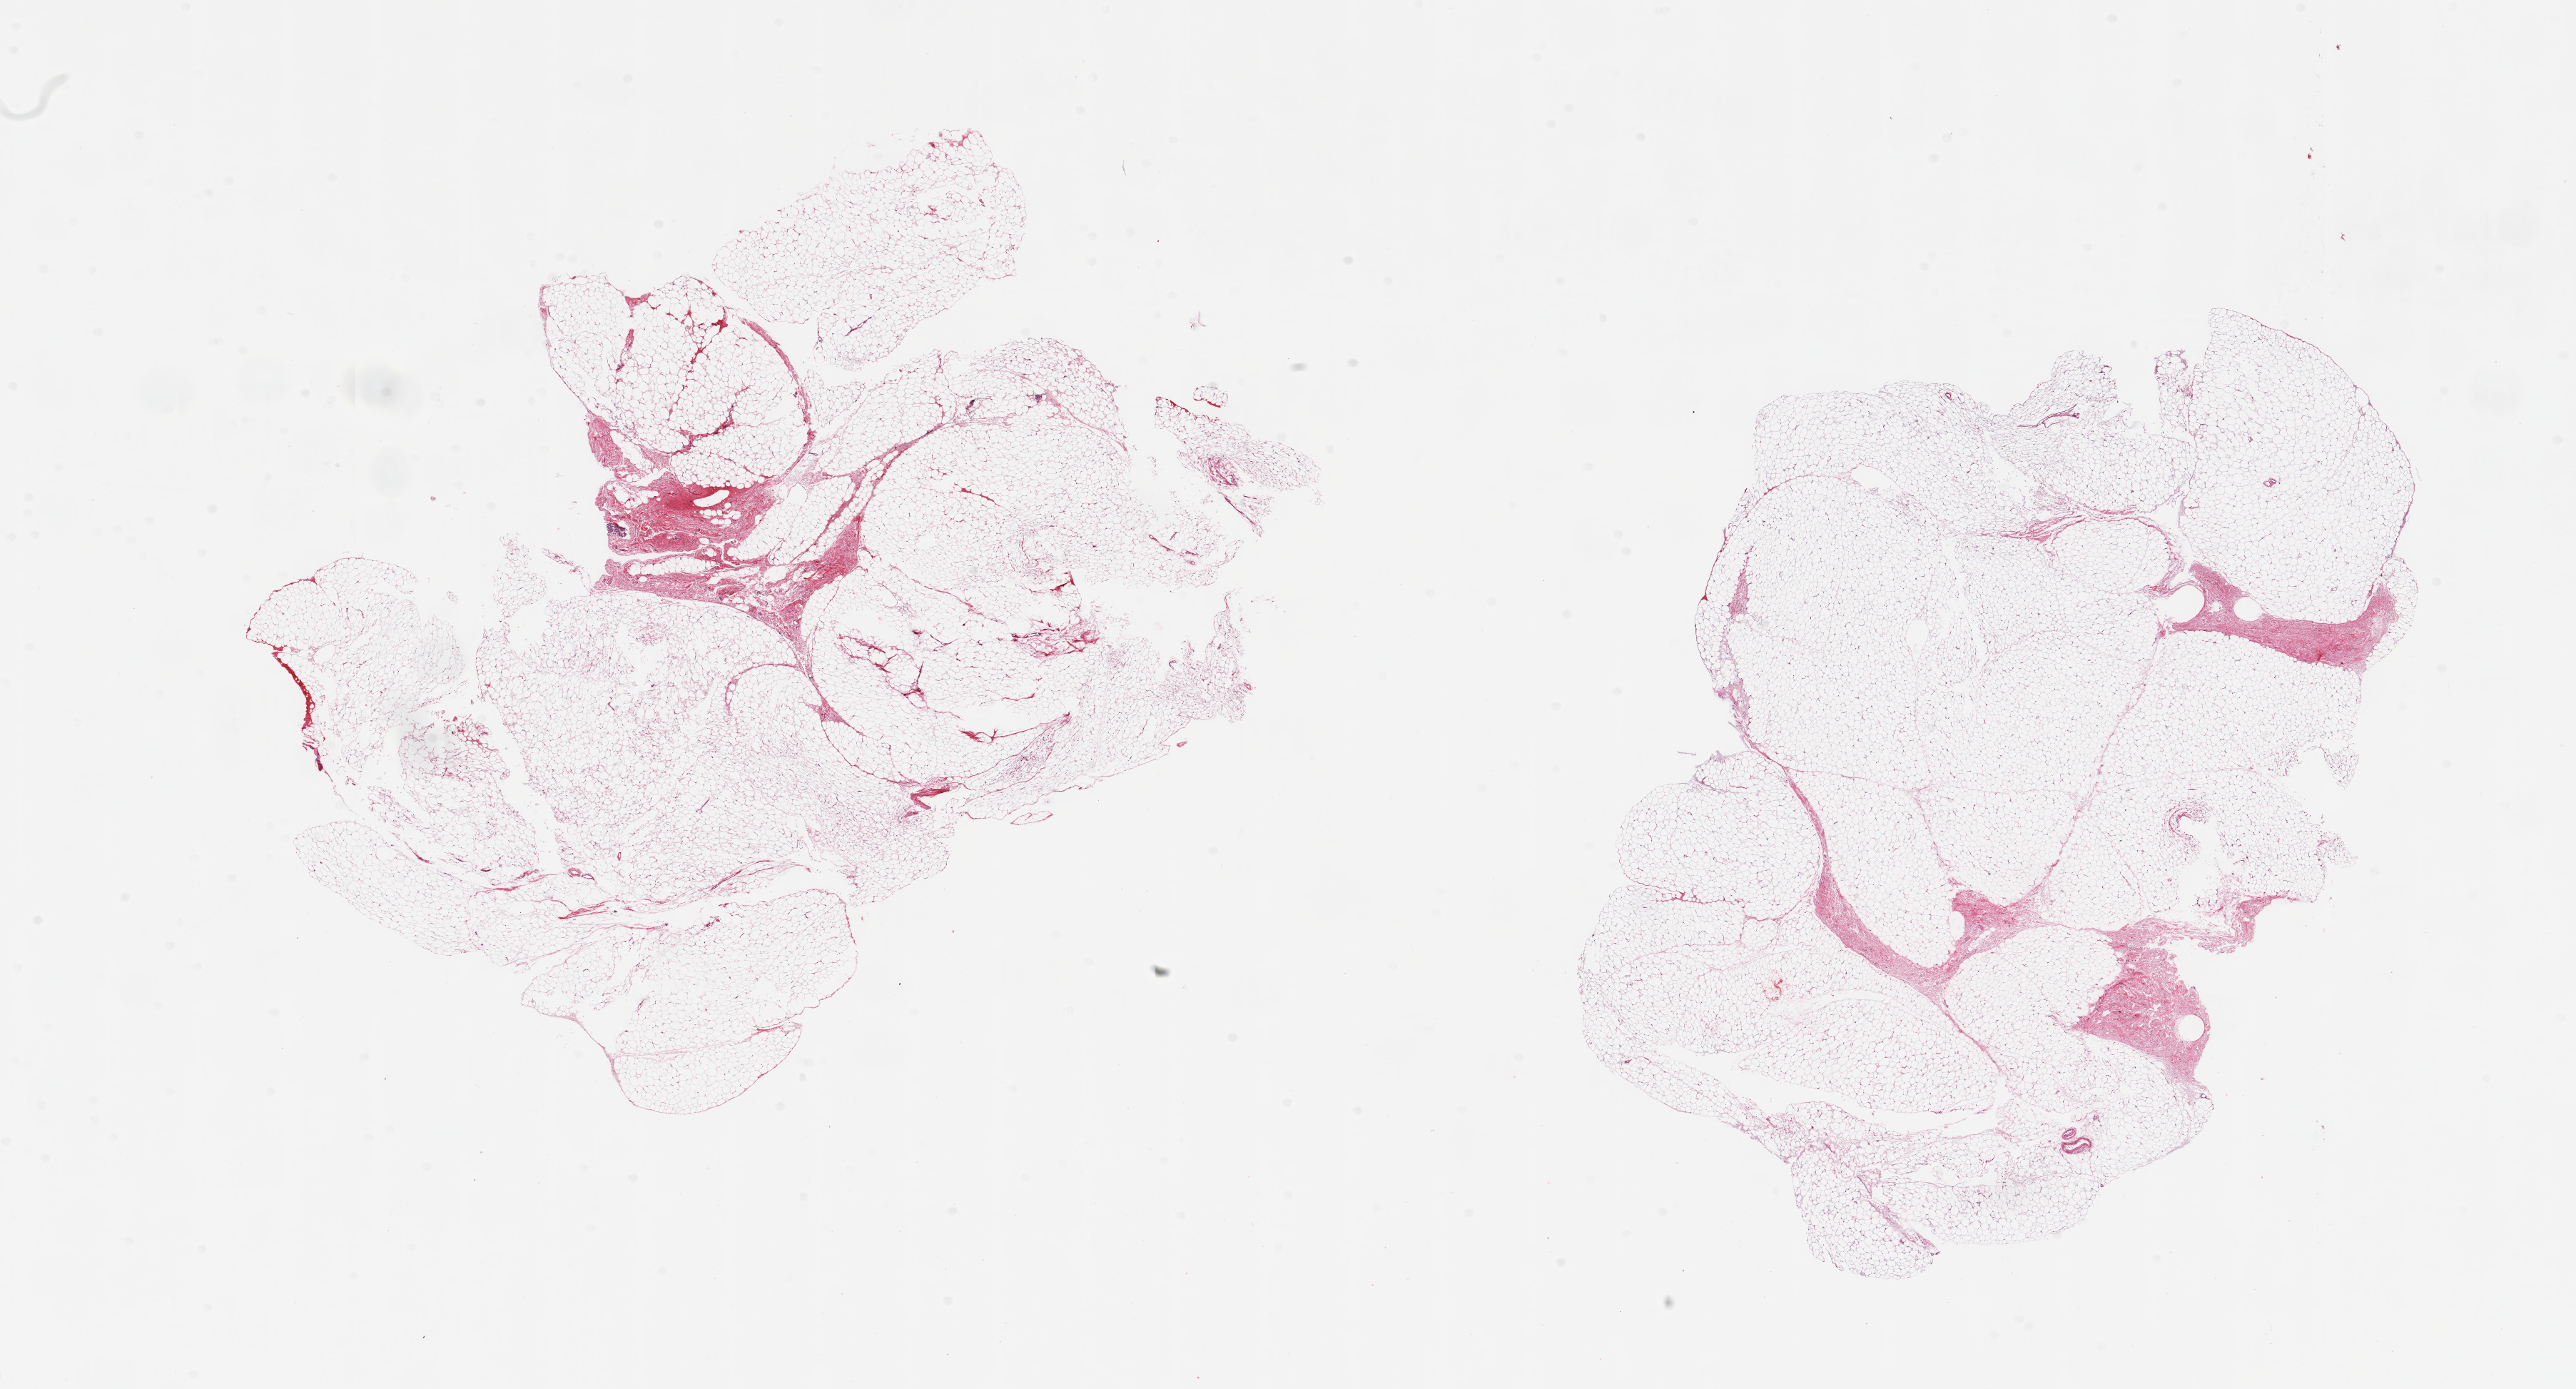
Whole-slide image, hematoxylin and eosin (H&E) stain, low-resolution overview of the scanned area, about 28.5 x 15.4 mm. PAXgene-fixed, paraffin-embedded tissue. Sampled site (target tissue): omentum. Donor tissue sample.
* review note (as recorded): 2 pieces, ~10% fascia/vascular elements